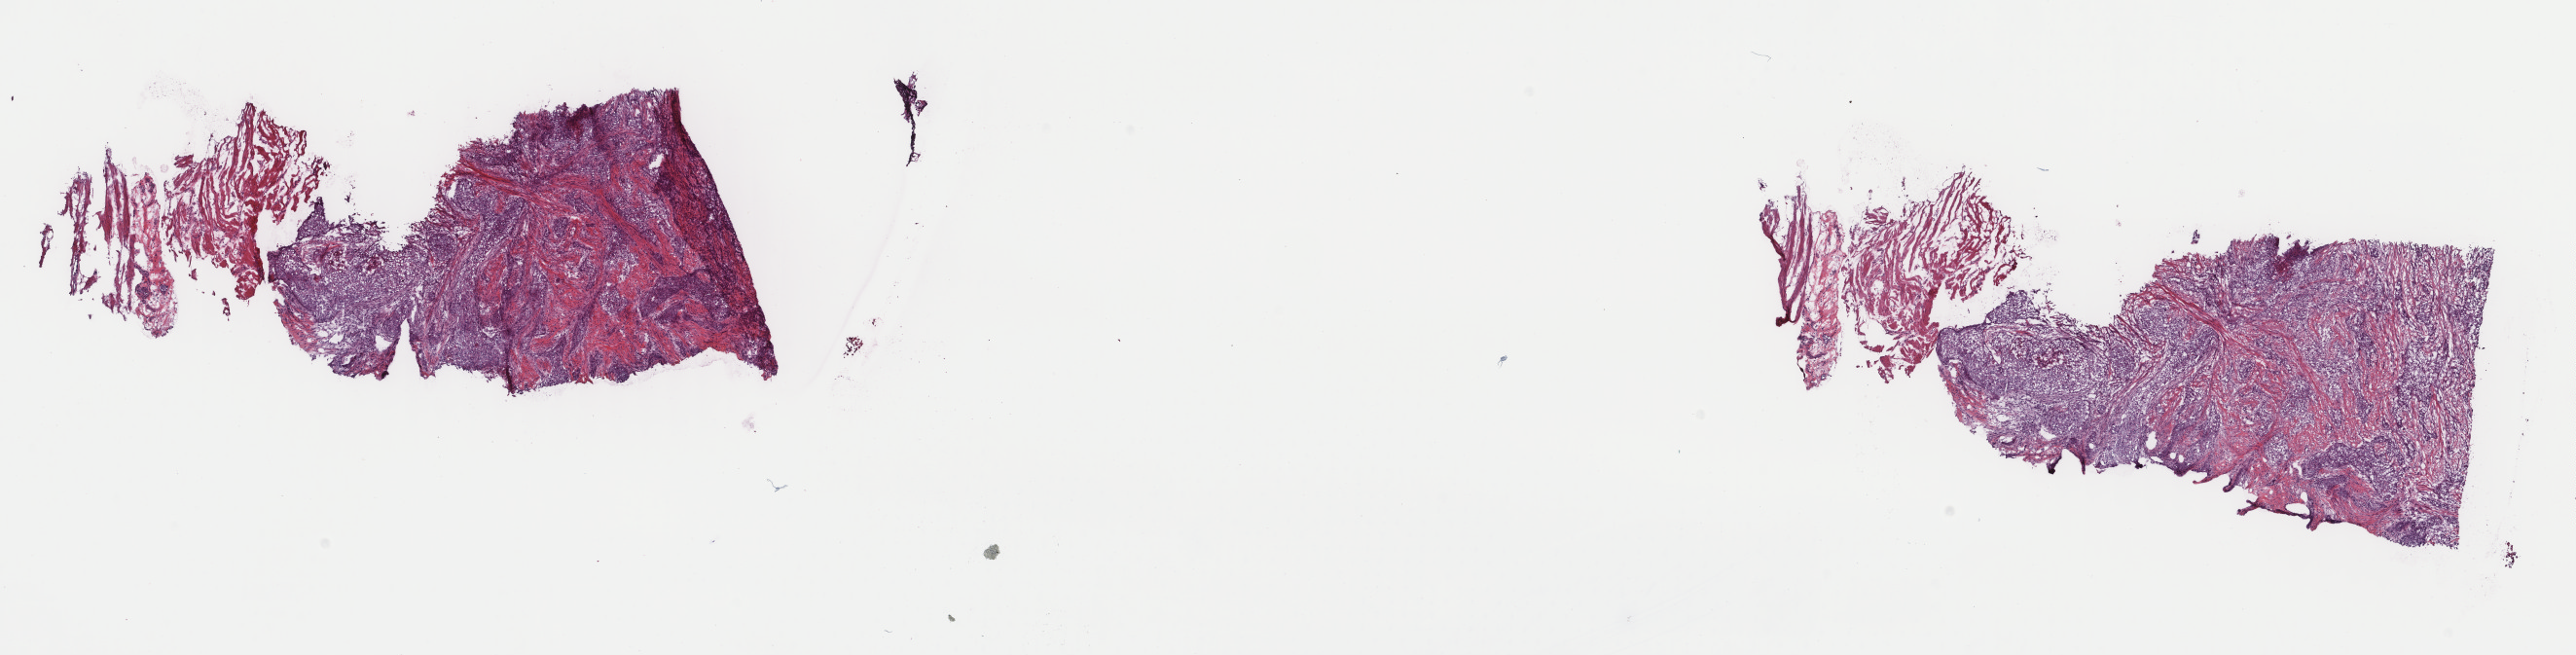
Digitized H&E tissue section (whole slide) — a low-resolution overview of the entire scanned area, about 21.0 x 5.3 mm (slide scanned at 40x). Frozen section. Primary tumour sample from the esophagus. Patient: male, age at initial diagnosis 49 years. Histologic grade: G2 (moderately differentiated). Slide review estimates, as recorded: tumour cells 80%, tumour nuclei 75%, normal cells 20%, stromal cells 0%, necrosis 0%. Infiltration values recorded for this section: lymphocyte infiltration 0%, monocyte infiltration 0%, neutrophil infiltration 0%.
AJCC pathologic stage: IIA (6th edition). Histologic diagnosis: Squamous cell carcinoma, NOS.